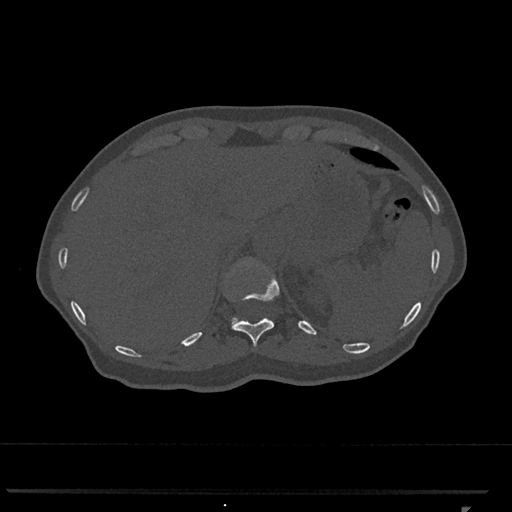
CT including the spine, one axial slice; position 505 of 793 along the scan axis; reconstruction kernel Br40s/3; 120 kVp; bone window (W 1800 / L 400 HU); 0.5 mm slice thickness; 512 × 512 image matrix, field of view 380 × 380 mm. Patient: female, 62 years. Case-level facts recorded for this patient, not image findings: primary cancer: renal.
Outlined on this slice (semi-automatically segmented with operator editing):
- T11 vertebra: bounding box [x1, y1, x2, y2] px = [231, 259, 280, 347]
- T12 vertebra: [231, 317, 271, 325]